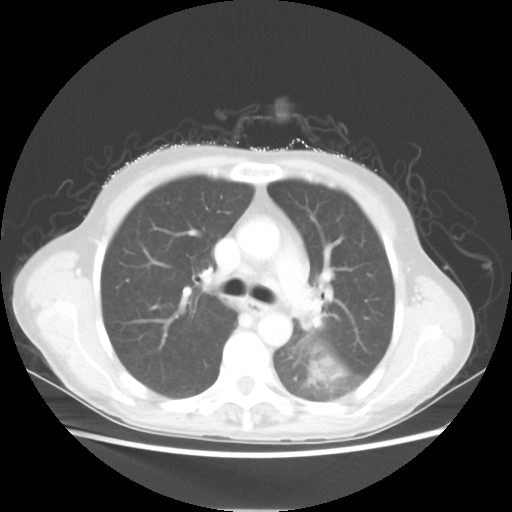
Chest CT, one axial slice; position 36 of 56 along the scan axis; 80 kVp; lung window (W 1500 / L -600 HU); 512 × 512 image matrix. Female patient, age 53 years. Case-level facts recorded for this patient, not image findings: clinical TNM (as recorded): T3 N0 M0.
Structures marked on this image (bounding box drawn by a radiologist):
- lung tumour (recorded histology: adenocarcinoma): bounding box [x1, y1, x2, y2] px = [311, 359, 342, 380]